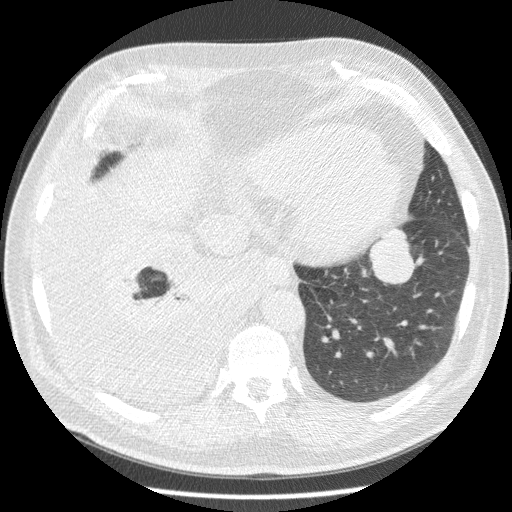
Low-dose screening chest CT, one axial slice; position 57 of 180 along the scan axis; 120 kVp; lung window (W 1500 / L -600 HU); 2.5 mm slice thickness; 512 × 512 image matrix, field of view 355 × 355 mm.
Outlined on this slice (expert manual segmentation):
- lesion 1 (tumor, lower lobe of left lung): bounding box [x1, y1, x2, y2] px = [369, 228, 421, 284]